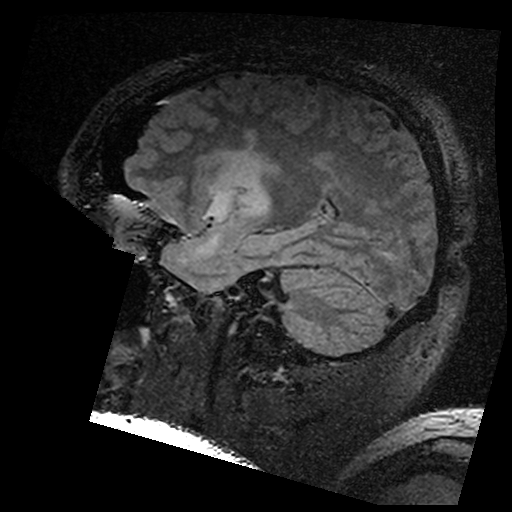
Brain MRI from a brain-tumour surgery series, one sagittal slice; T2 FLAIR; 512 × 512 image matrix, field of view 250 × 250 mm. Case-level facts recorded for this patient, not image findings: histopathology: Astrocytoma; WHO grade: 3; IDH mutation: yes; tumour location: Left Insular.
Outlined on this slice (outlined manually by an expert reader):
- residual tumour: bounding box <202,146,280,201> (left, top, right, bottom; pixels)